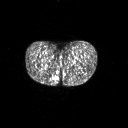
FDG PET of an extremity soft-tissue mass (from a PET/CT study), one axial slice. 3.27 mm slice thickness. 128 × 128 image matrix, field of view 700 × 700 mm. Female patient, age 17 years. From the clinical record (not read from this slice): histological type: epithelioid sarcoma; grade: intermediate; site of the primary tumour: right buttock.
Annotated regions visible in this slice (expert contour drawn on MRI and transferred to this co-registered scan by the dataset authors):
- gross tumour volume including surrounding oedema: bounding box <51,76,59,85> (left, top, right, bottom; pixels)